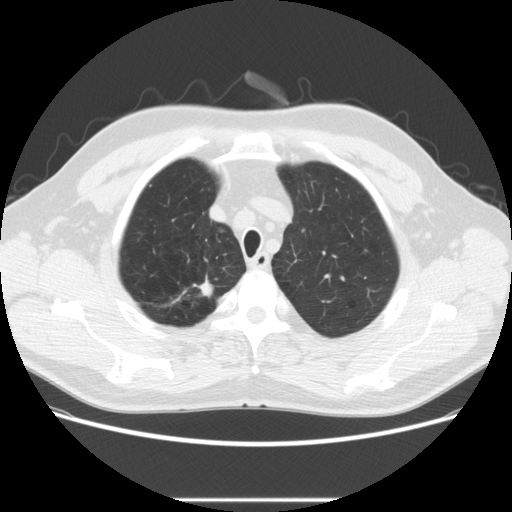
Axial slice from a low-dose chest CT screening exam; first (baseline) screen; lung window (W 1500 / L -600 HU); 2.5 mm slice thickness; standard (soft-tissue) reconstruction kernel (STANDARD); slice 40 of 270 in the series. Male, age 64 years at enrolment. Former smoker at enrolment.
Expert reader's lesion annotation, bounding box (x1, y1, x2, y2) in pixels: (173, 278, 221, 307). The screening reader recorded 2 non-calcified nodules or masses ≥4 mm on this exam; which of them this box marks is not recorded. Later outcome: lung cancer diagnosed 753 days after this screen (after the third annual screen) — adenocarcinoma, NOS, right upper lobe, moderately differentiated (G2), stage IA (AJCC 6th edition), 14 mm at pathology.